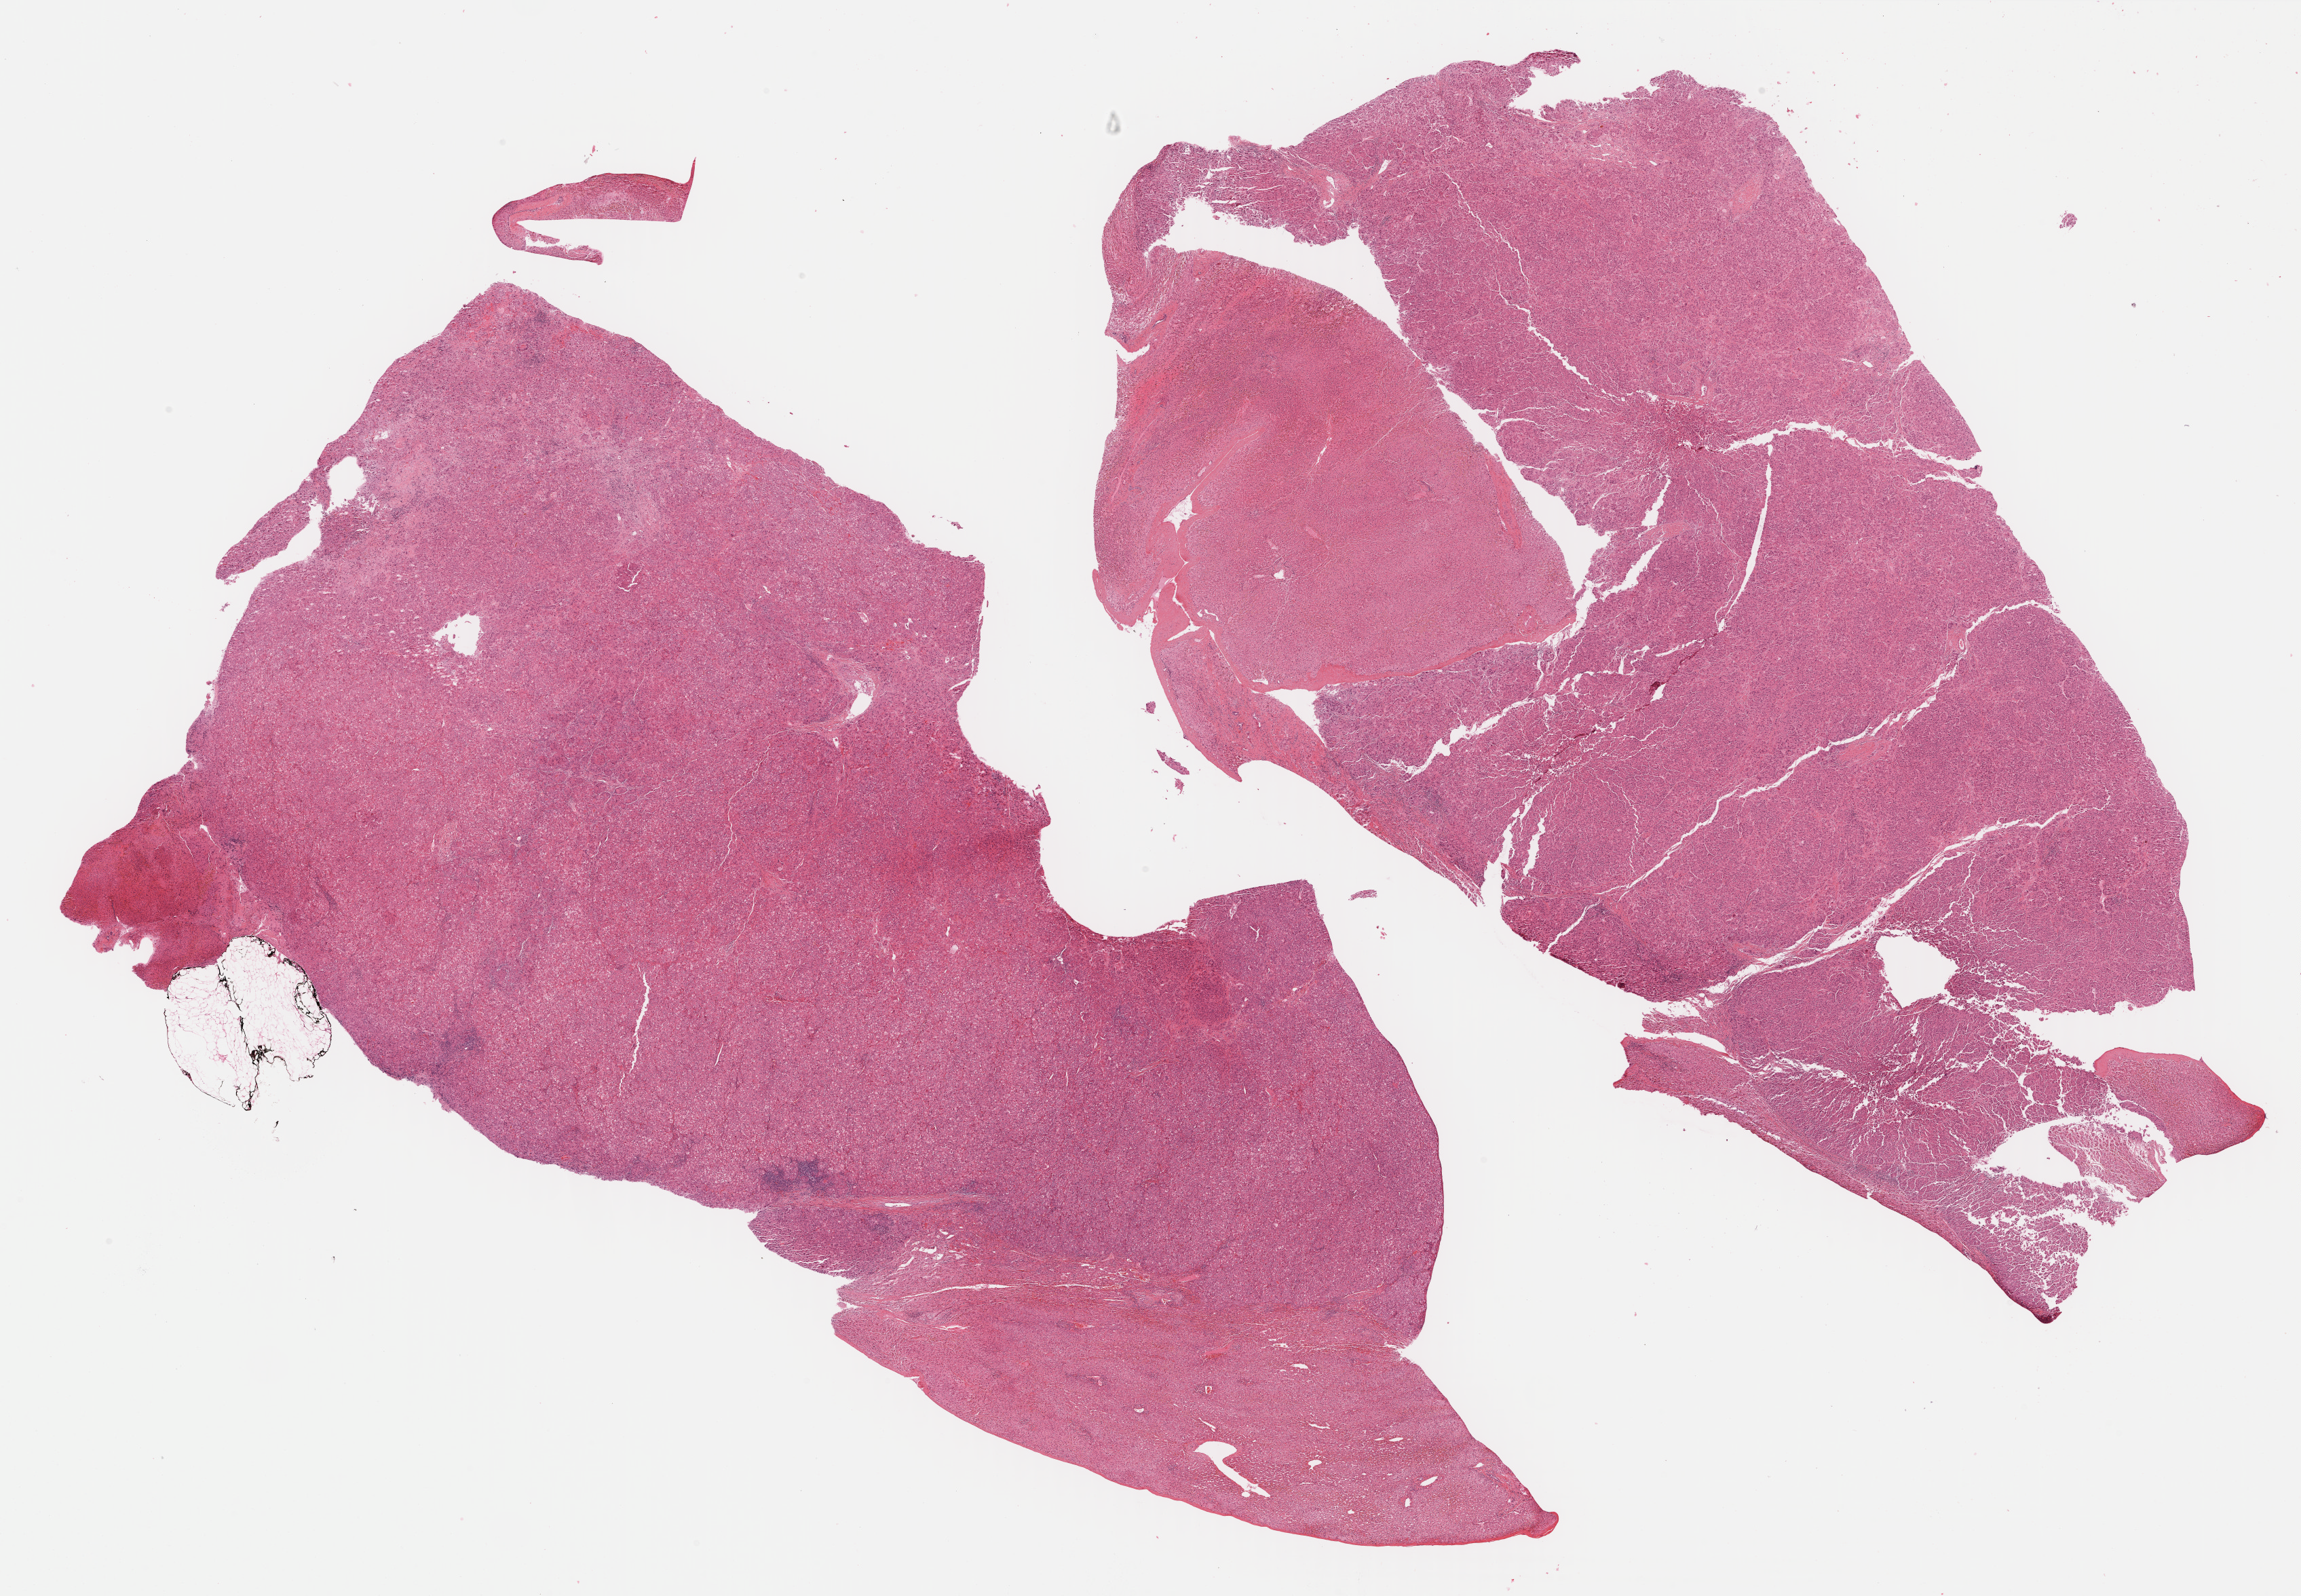
Digitized H&E-stained tissue section (whole slide) — whole scanned area (about 27.4 x 19.0 mm, from a 40x scan) shown as a low-resolution overview, formalin-fixed paraffin-embedded (FFPE) diagnostic section, sample: primary tumour, liver. Female, age 78 years at initial diagnosis. Histologic grade: G2 (moderately differentiated).
Diagnosis: Hepatocellular carcinoma, NOS. AJCC pathologic stage: I (5th edition).